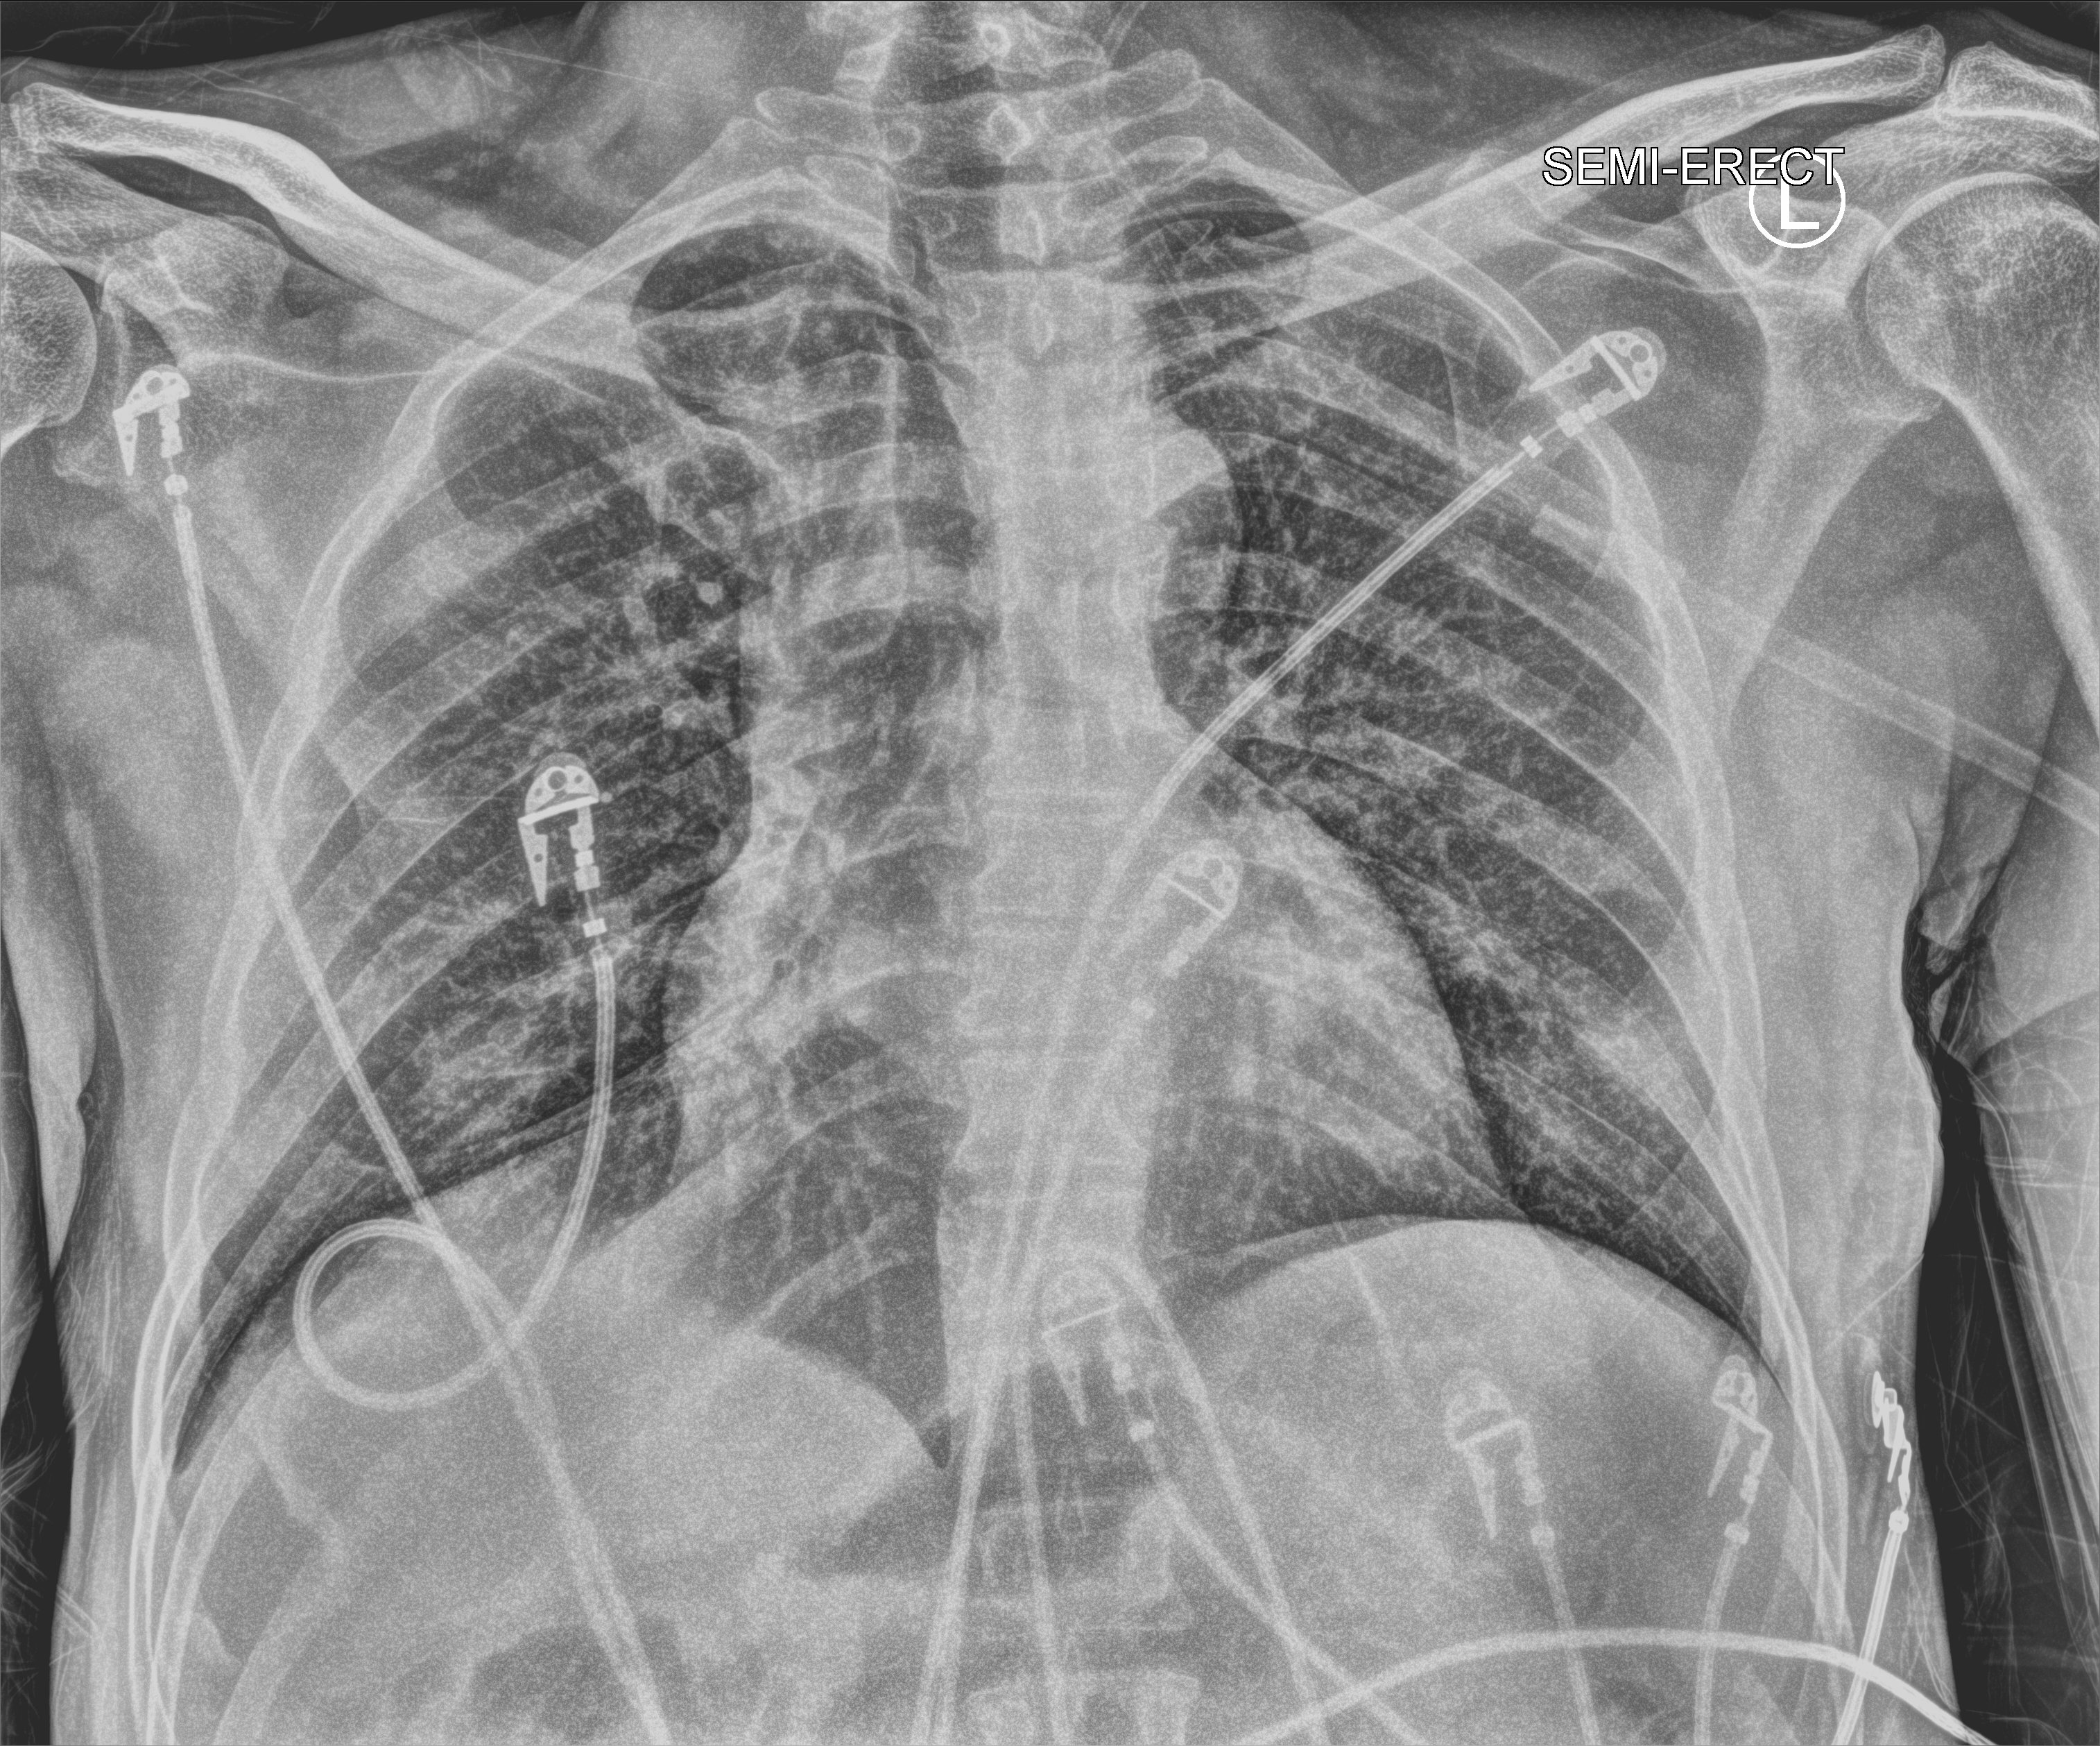
Bedside chest radiograph (computed radiography), anteroposterior (AP) projection. Patient hospitalised with COVID-19; male, aged 18–59 years.
From the hospital-stay record, not from the radiograph (when in the stay this image was taken is not recorded):
- length of hospital stay: 41 days